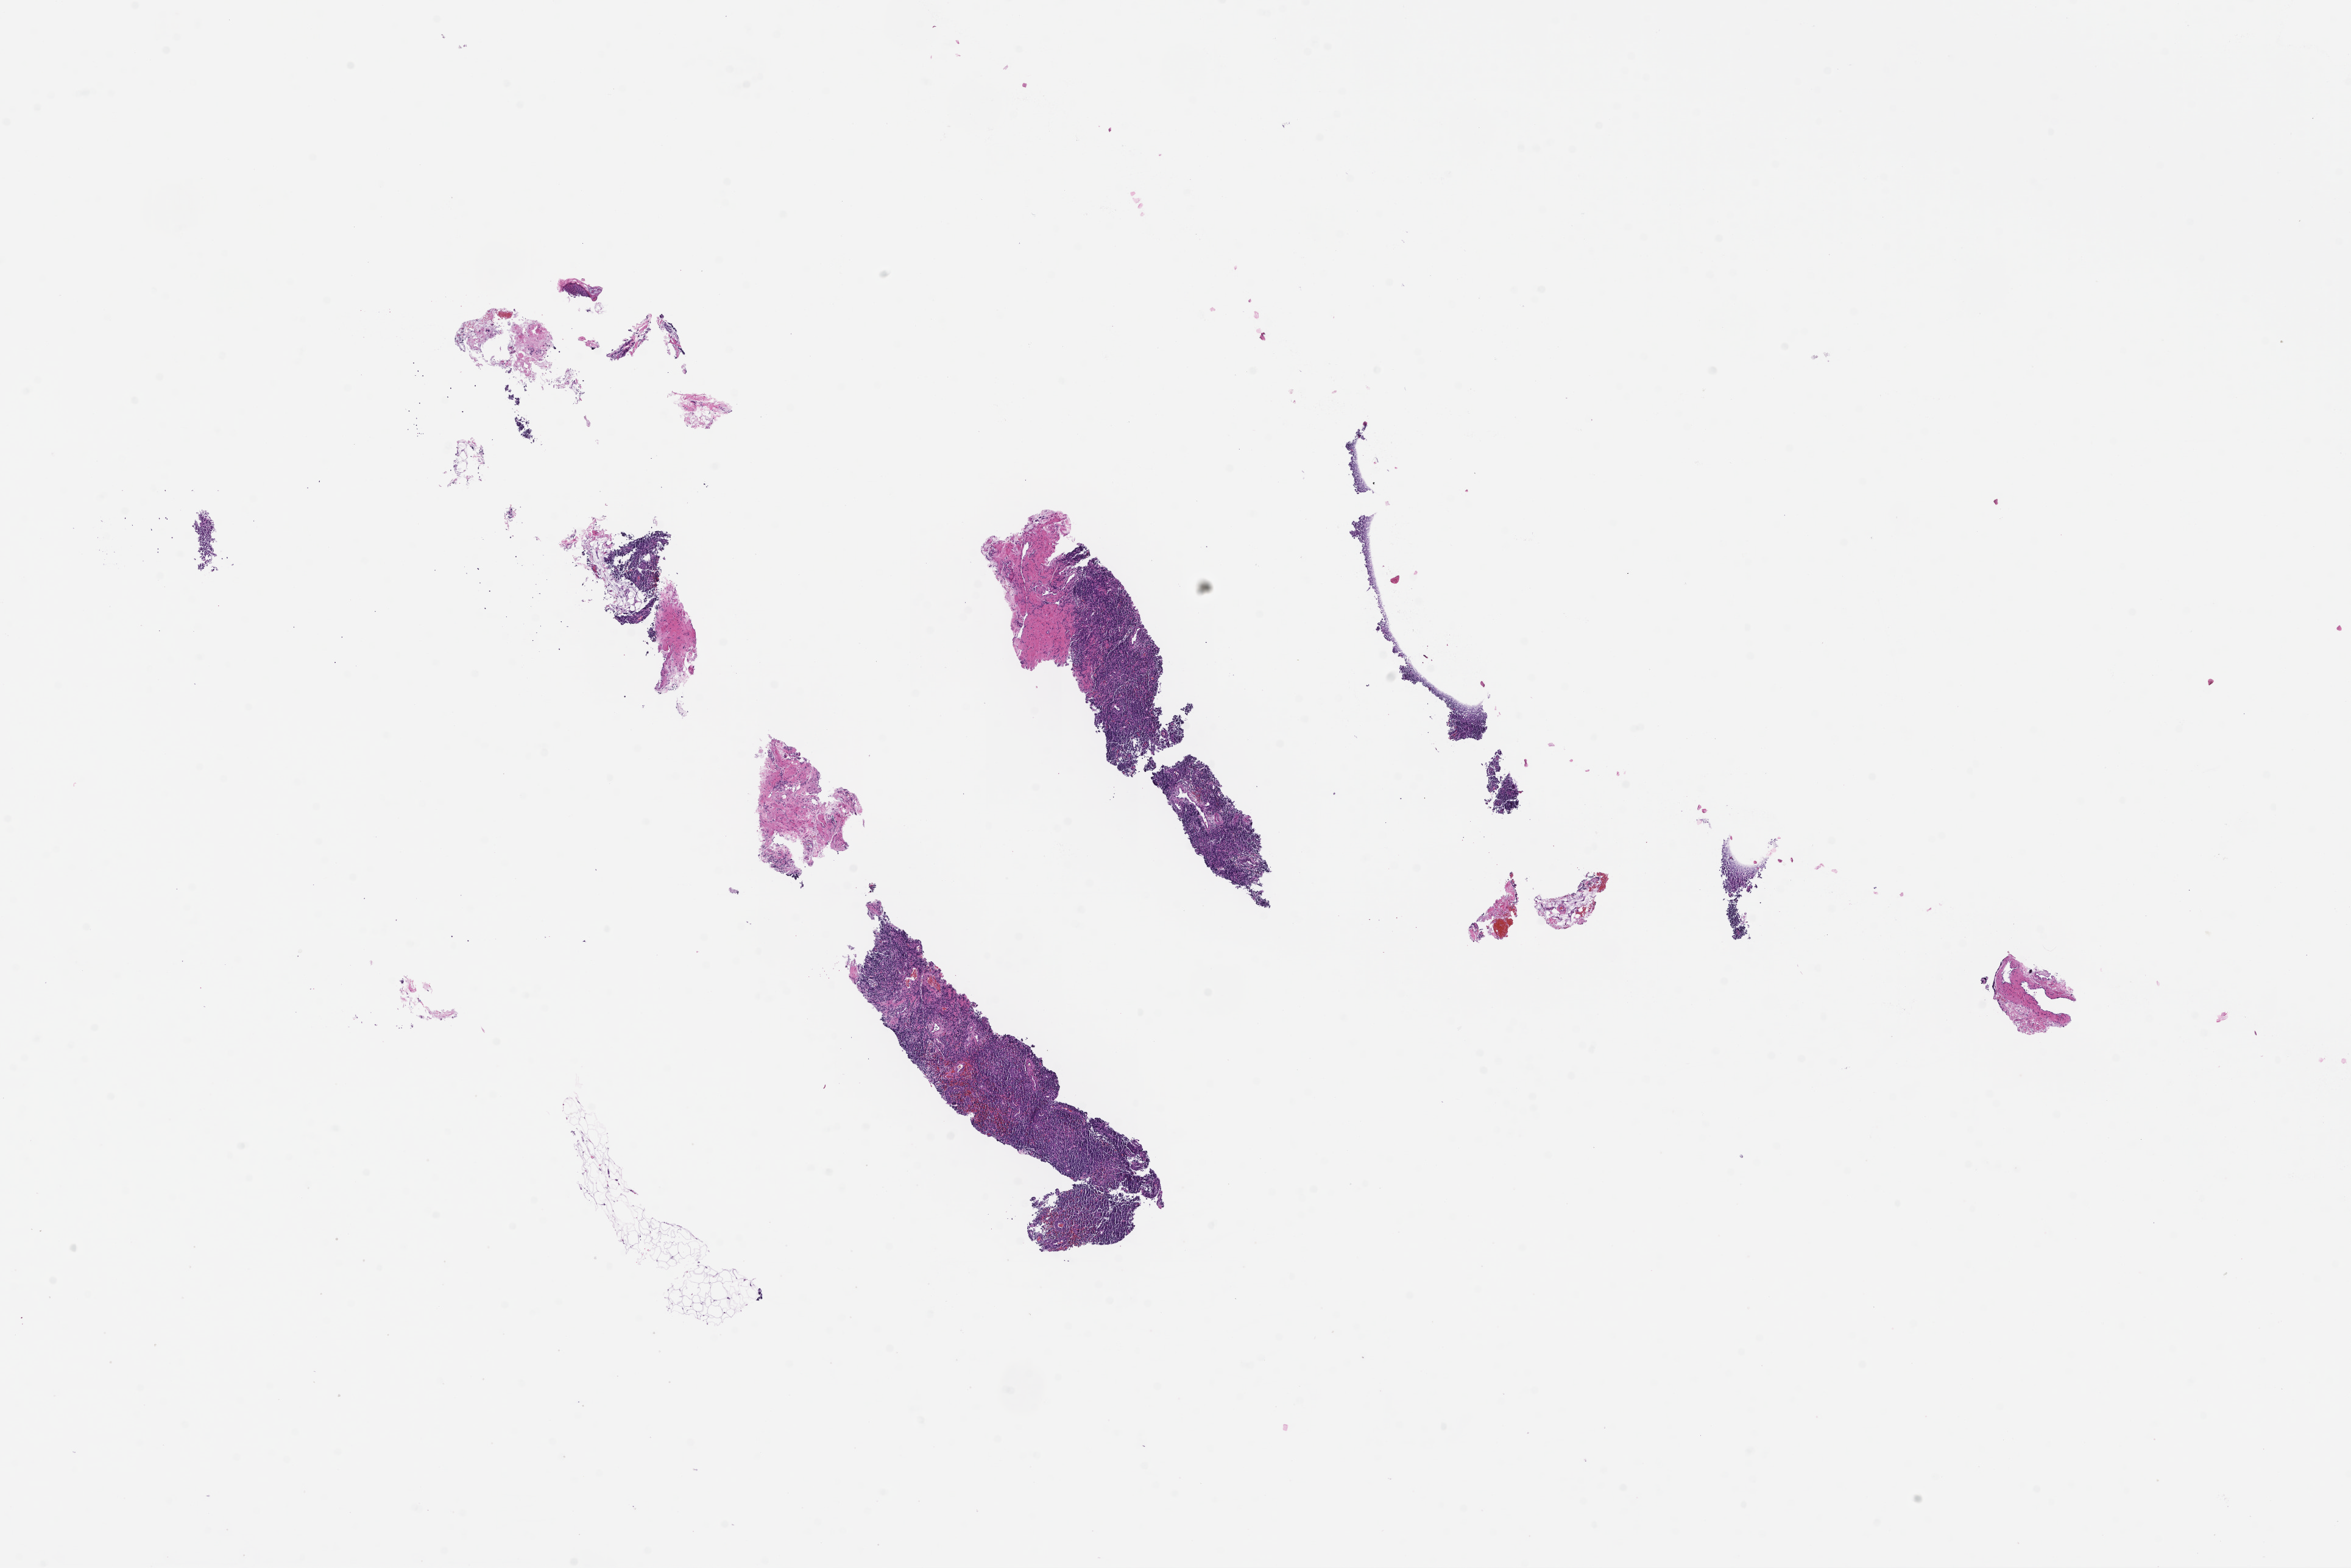
Whole-slide image, H&E stain, whole scanned area (about 15.6 x 10.4 mm) shown as a low-resolution overview. FFPE section. Patient sex: male.
• this section: metastasis (sampled organ not recorded)
• patient diagnosis (primary): Melanoma